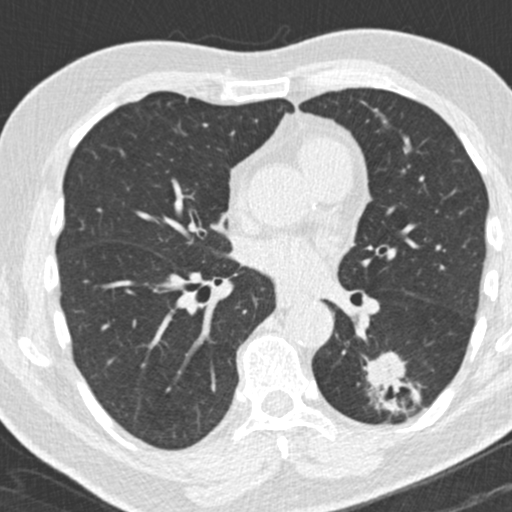
Low-dose screening chest CT, one axial slice. 120 kVp. Lung window (W 1500 / L -600 HU). 2 mm slice thickness. 512 × 512 image matrix, field of view 300 × 300 mm.
Outlined on this slice (expert manual segmentation):
- lesion 1 (tumor, lower lobe of left lung): bounding box [x1, y1, x2, y2] px = [366, 352, 405, 388]